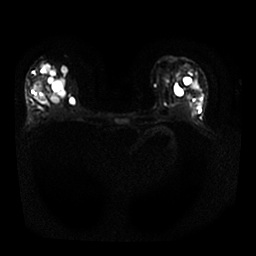
Breast MRI, one axial slice. Position 15 of 25 along the scan axis. Diffusion-weighted series; image 2 of 4 stored at this slice position (different b-values; order by instance number). 1.5 T. 256 × 256 image matrix. Female patient.
Annotated regions visible in this slice (outlined manually by an expert reader):
- tumour on diffusion-weighted imaging: box from (x=35, y=78) to (x=52, y=106) px